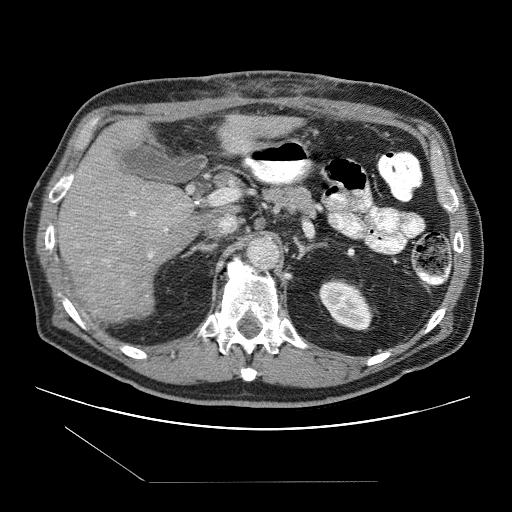
Contrast-enhanced abdominal CT (liver protocol), one axial slice. Position 53 of 109 along the scan axis. Reconstruction kernel STANDARD. One of 2 acquisitions stored at this slice position. Soft-tissue window (W 400 / L 40 HU). 2.5 mm slice thickness. 512 × 512 image matrix. From the clinical record (not read from this slice): diagnosis: hepatocellular carcinoma (patient treated with transarterial chemoembolisation; whether this scan precedes or follows treatment is not stated here); TNM stage (as recorded): Stage-IIIB.
Outlined on this slice (semi-automatically segmented with operator editing):
- liver parenchyma outside the tumour (the mass and vessels are separate outlines, so this box may not span the whole liver): box from (x=56, y=114) to (x=302, y=320) px
- liver vessels: (x=119, y=147)–(x=245, y=258)